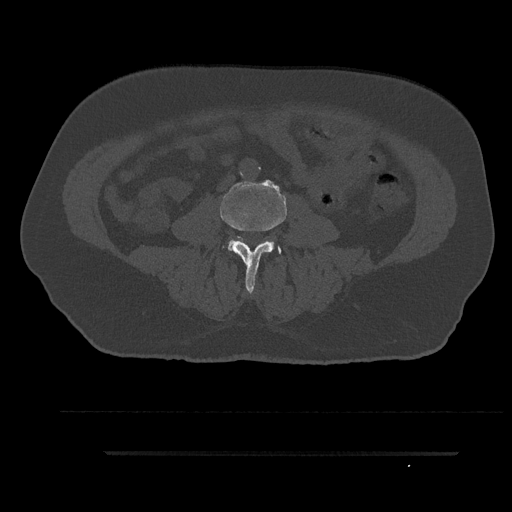
CT including the spine, one axial slice. Slice 22 of 797 in the series (ordered by position). Reconstruction kernel Br40s/3. 120 kVp. Bone window (W 1800 / L 400 HU). 512 × 512 image matrix, field of view 432 × 432 mm. Patient: male, 63 years. From the clinical record (not read from this slice): primary cancer: renal; vertebrae with lytic lesions (as recorded): T8.
Outlined on this slice (semi-automatically segmented with operator editing):
- L3 vertebra: box from (x=220, y=185) to (x=287, y=294) px
- L4 vertebra: (x=222, y=241)–(x=281, y=256)